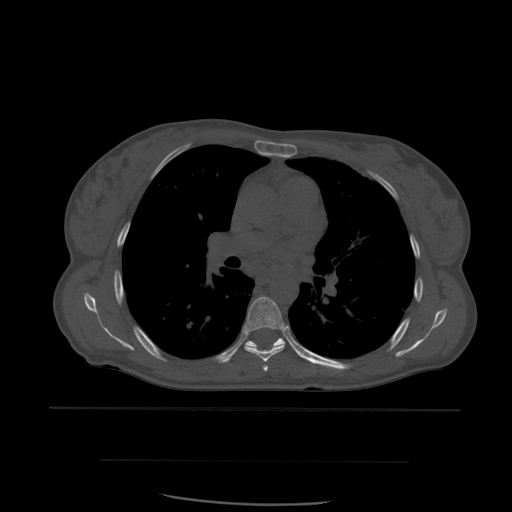
CT including the spine, one axial slice. Slice 387 of 574 in the series (ordered by position). Bone window (W 1800 / L 400 HU). 1.25 mm slice thickness. 512 × 512 image matrix, field of view 392 × 392 mm. Patient age 48 years. From the clinical record (not read from this slice): primary cancer: lung.
Annotated regions visible in this slice (semi-automatic segmentation, software-assisted and operator-edited):
- T5 vertebra: bounding box (x1, y1, x2, y2) in pixels: (263, 365, 269, 372)
- T6 vertebra: (244, 297, 289, 363)
- T7 vertebra: (246, 338, 287, 348)